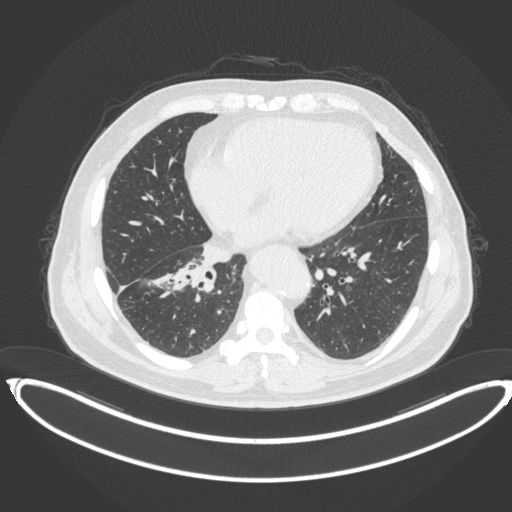
Chest CT, one axial slice; slice 158 of 383 in the series (ordered by position); reconstruction kernel B31f; lung window (W 1500 / L -600 HU); 1 mm slice thickness; 512 × 512 image matrix. Male patient, age 61 years. Case-level facts recorded for this patient, not image findings: clinical TNM (as recorded): T1b N1 M0.
Annotated regions visible in this slice (bounding box drawn by a radiologist):
- lung tumour (recorded histology: squamous cell carcinoma): bounding box (x1, y1, x2, y2) in pixels: (173, 255, 219, 295)